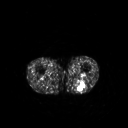
FDG PET of an extremity soft-tissue mass (from a PET/CT study), one axial slice. Slice 200 of 267 in the series (ordered by position). 128 × 128 image matrix. Male patient, age 54 years. Case-level facts recorded for this patient, not image findings: histological type: synovial sarcoma; site of the primary tumour: left poplietal fossa.
Outlined on this slice (expert contour drawn on MRI and transferred to this co-registered scan by the dataset authors):
- gross tumour volume (mass): box from (x=76, y=81) to (x=85, y=91) px